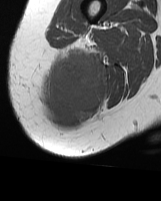
MRI of an extremity soft-tissue mass, one axial slice; position 17 of 70 along the scan axis; MR volume resampled by the dataset authors to the PET/CT grid (not the native acquisition matrix); 161 × 201 image matrix. Female patient. Case-level facts recorded for this patient, not image findings: histological type: synovial sarcoma; grade: intermediate; site of the primary tumour: right buttock.
Outlined on this slice (expert contour drawn on MRI and transferred to this co-registered scan by the dataset authors):
- gross tumour volume including surrounding oedema: bounding box [x1, y1, x2, y2] px = [40, 47, 103, 126]
- gross tumour volume (mass): [44, 54, 102, 126]